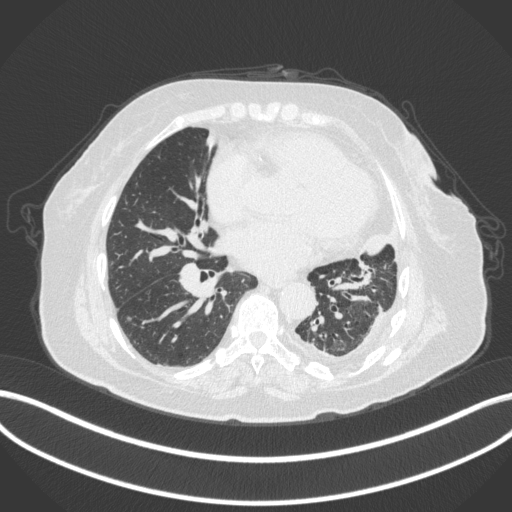
Chest CT, one axial slice; position 163 of 399 along the scan axis; reconstruction kernel B31f; 120 kVp; lung window (W 1500 / L -600 HU); 1 mm slice thickness; 512 × 512 image matrix, field of view 400 × 400 mm. Patient: female, 75 years. Case-level facts recorded for this patient, not image findings: clinical TNM (as recorded): T3 N3 M1.
Structures marked on this image (rectangle marked by the reading radiologist):
- lung tumour (recorded histology: adenocarcinoma): bounding box (x1, y1, x2, y2) in pixels: (361, 227, 386, 261)